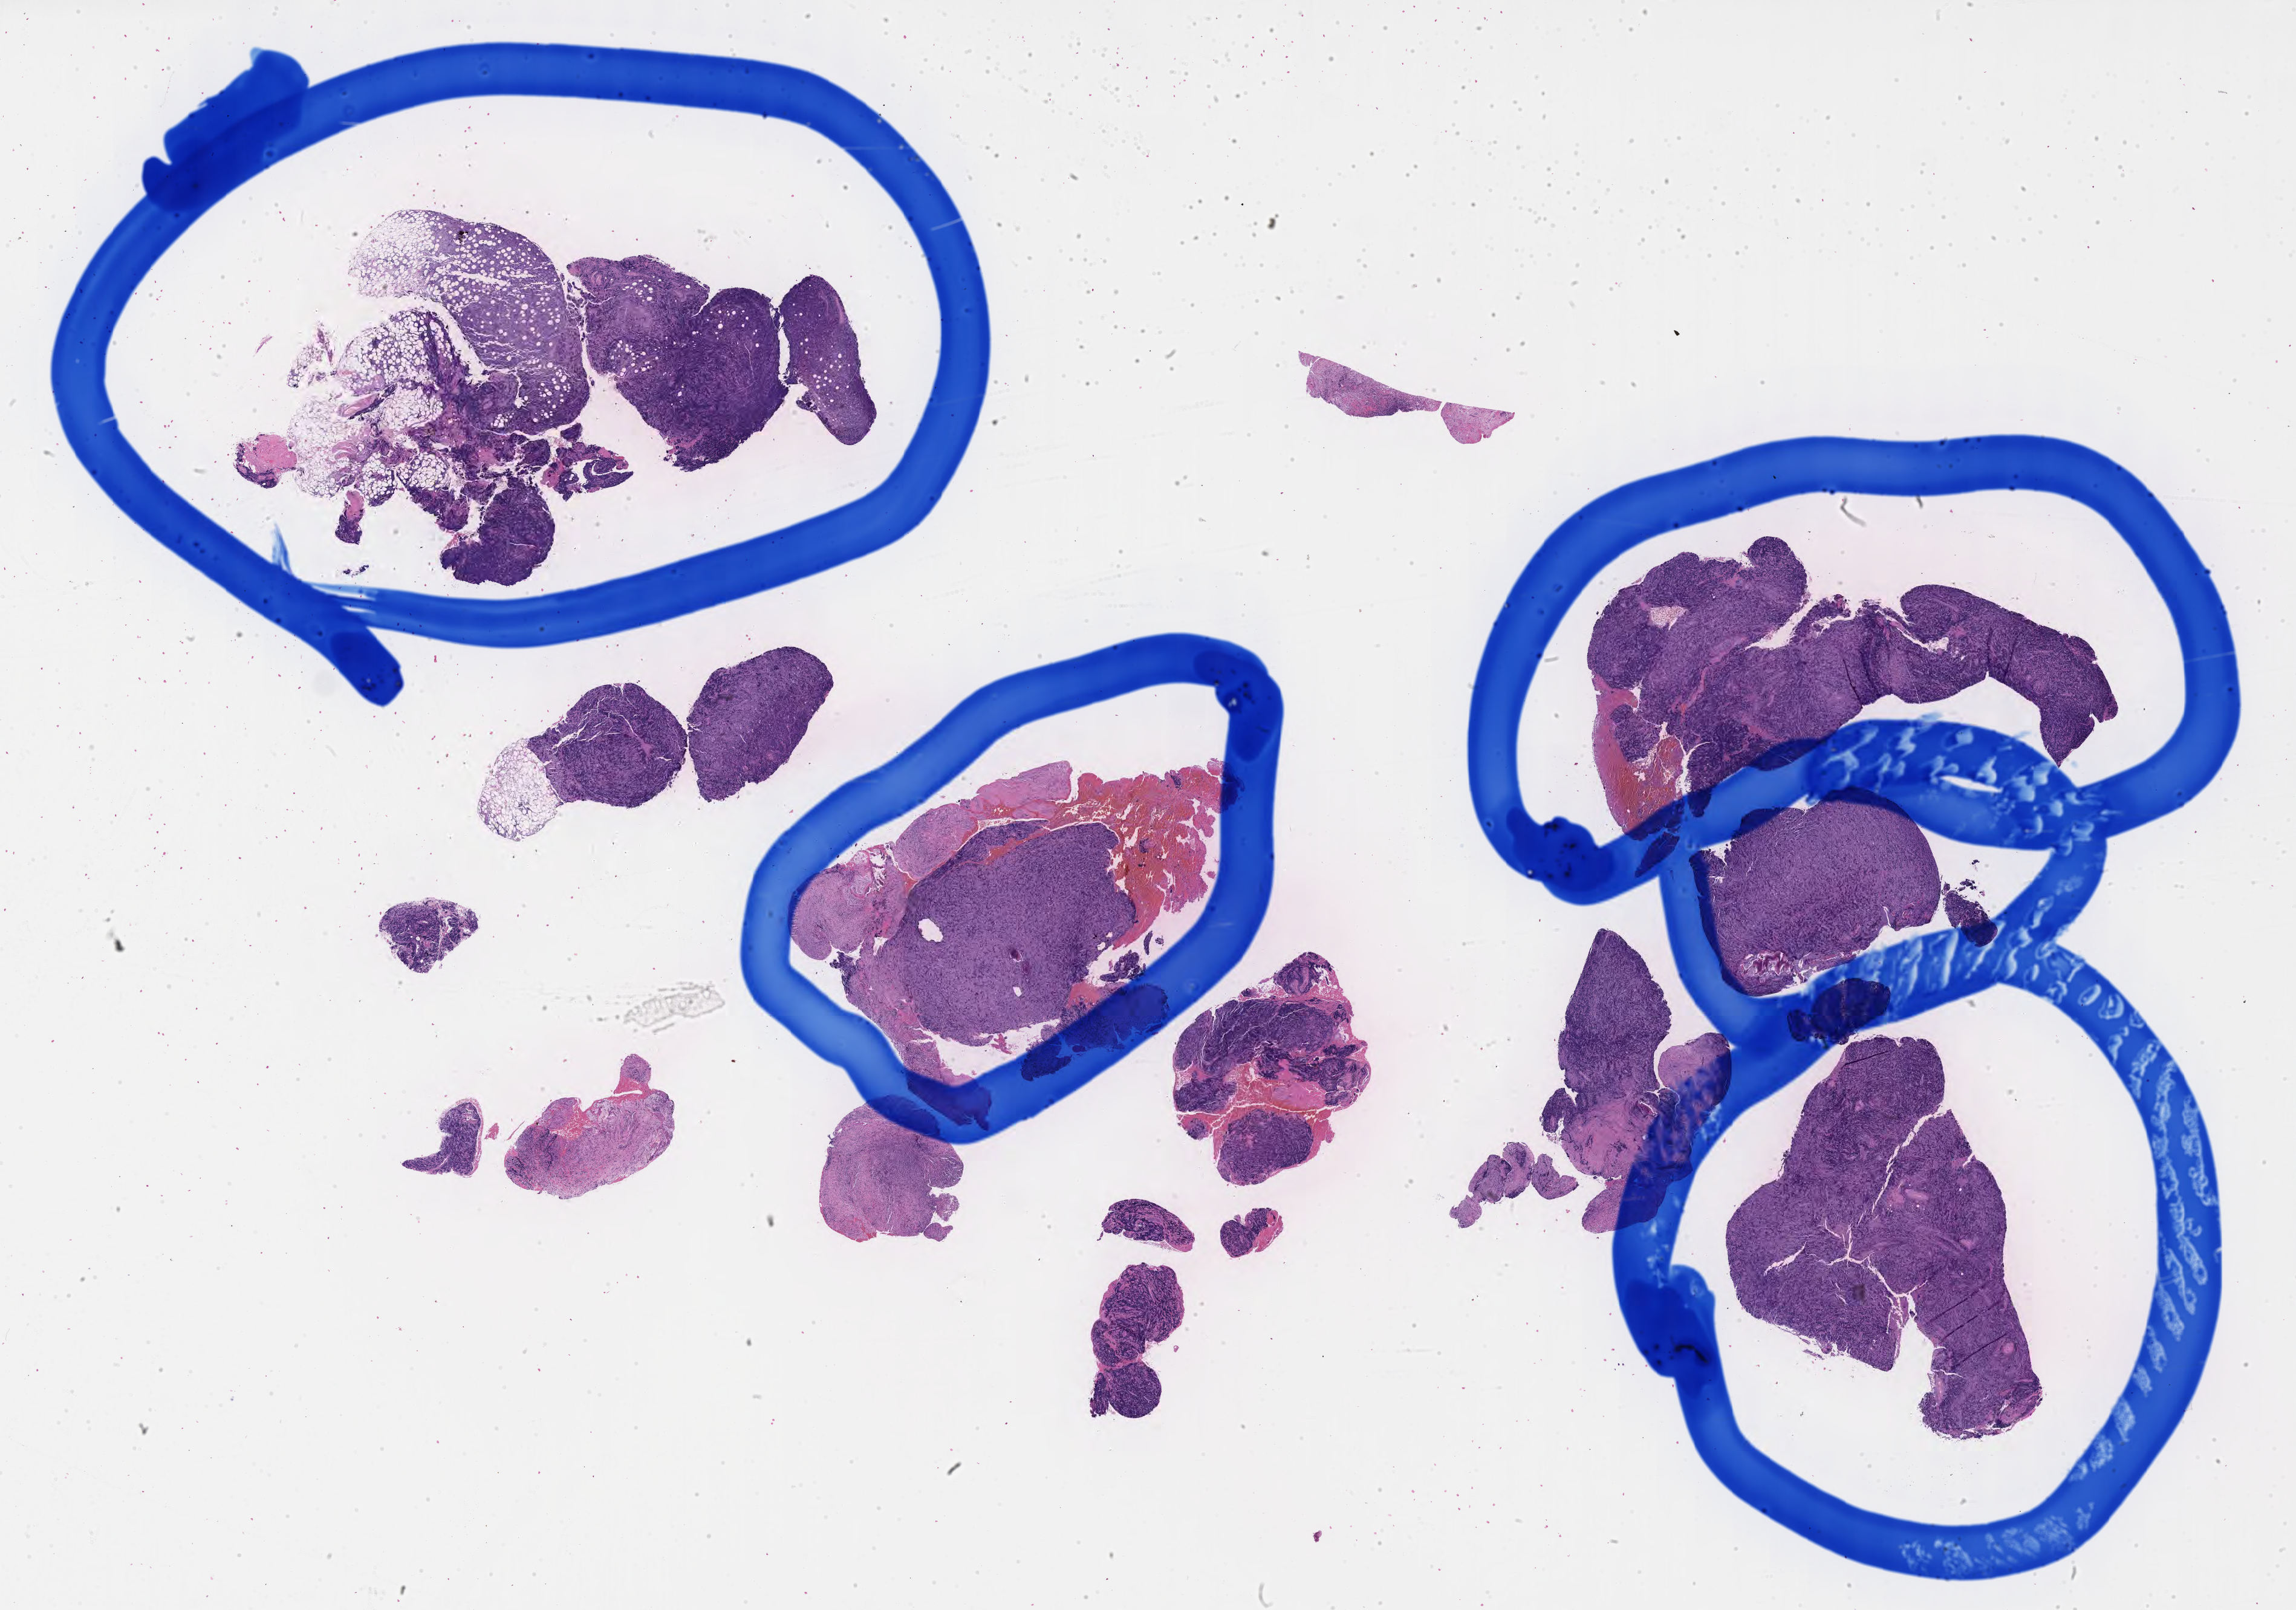
Digitized H&E-stained section — whole scanned area (about 30.7 x 21.5 mm) shown as a low-resolution overview; tumor tissue. Male patient, 45 years old.
Diagnosis: Diffuse large B-cell lymphoma, NOS.